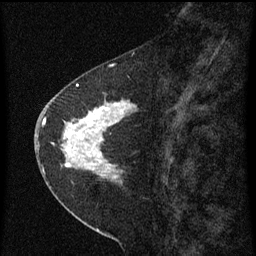
Breast MRI (dynamic contrast-enhanced), one sagittal slice; slice 27 of 60 in the series (ordered by position); dynamic contrast-enhanced series, image 2 of 3 at this slice position (ordered by acquisition); 1.5 T; TE 4.2 ms, TR 8 ms; 2 mm slice thickness; 256 × 256 image matrix, field of view 180 × 180 mm. Female patient, age 47 years.
Structures marked on this image (semi-automatic segmentation, software-assisted and operator-edited):
- analysis volume of interest (the breast-tissue region the enhancement analysis was run in; not a lesion): bounding box [x1, y1, x2, y2] px = [44, 84, 139, 199]
- tumour enhancement mask (voxels above the 70 % enhancement threshold inside the analysis volume of interest): [44, 84, 137, 179]